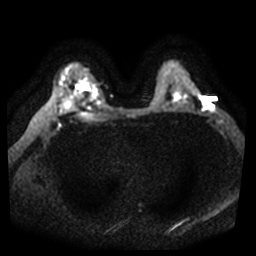
Breast MRI, one axial slice. Slice 30 of 44 in the series (ordered by position). Diffusion-weighted series; image 2 of 4 stored at this slice position (different b-values; order by instance number). 3 T. 256 × 256 image matrix, field of view 360 × 360 mm. Female patient.
Structures marked on this image (outlined manually by an expert reader):
- tumour on diffusion-weighted imaging: bounding box [x1, y1, x2, y2] px = [202, 101, 212, 109]